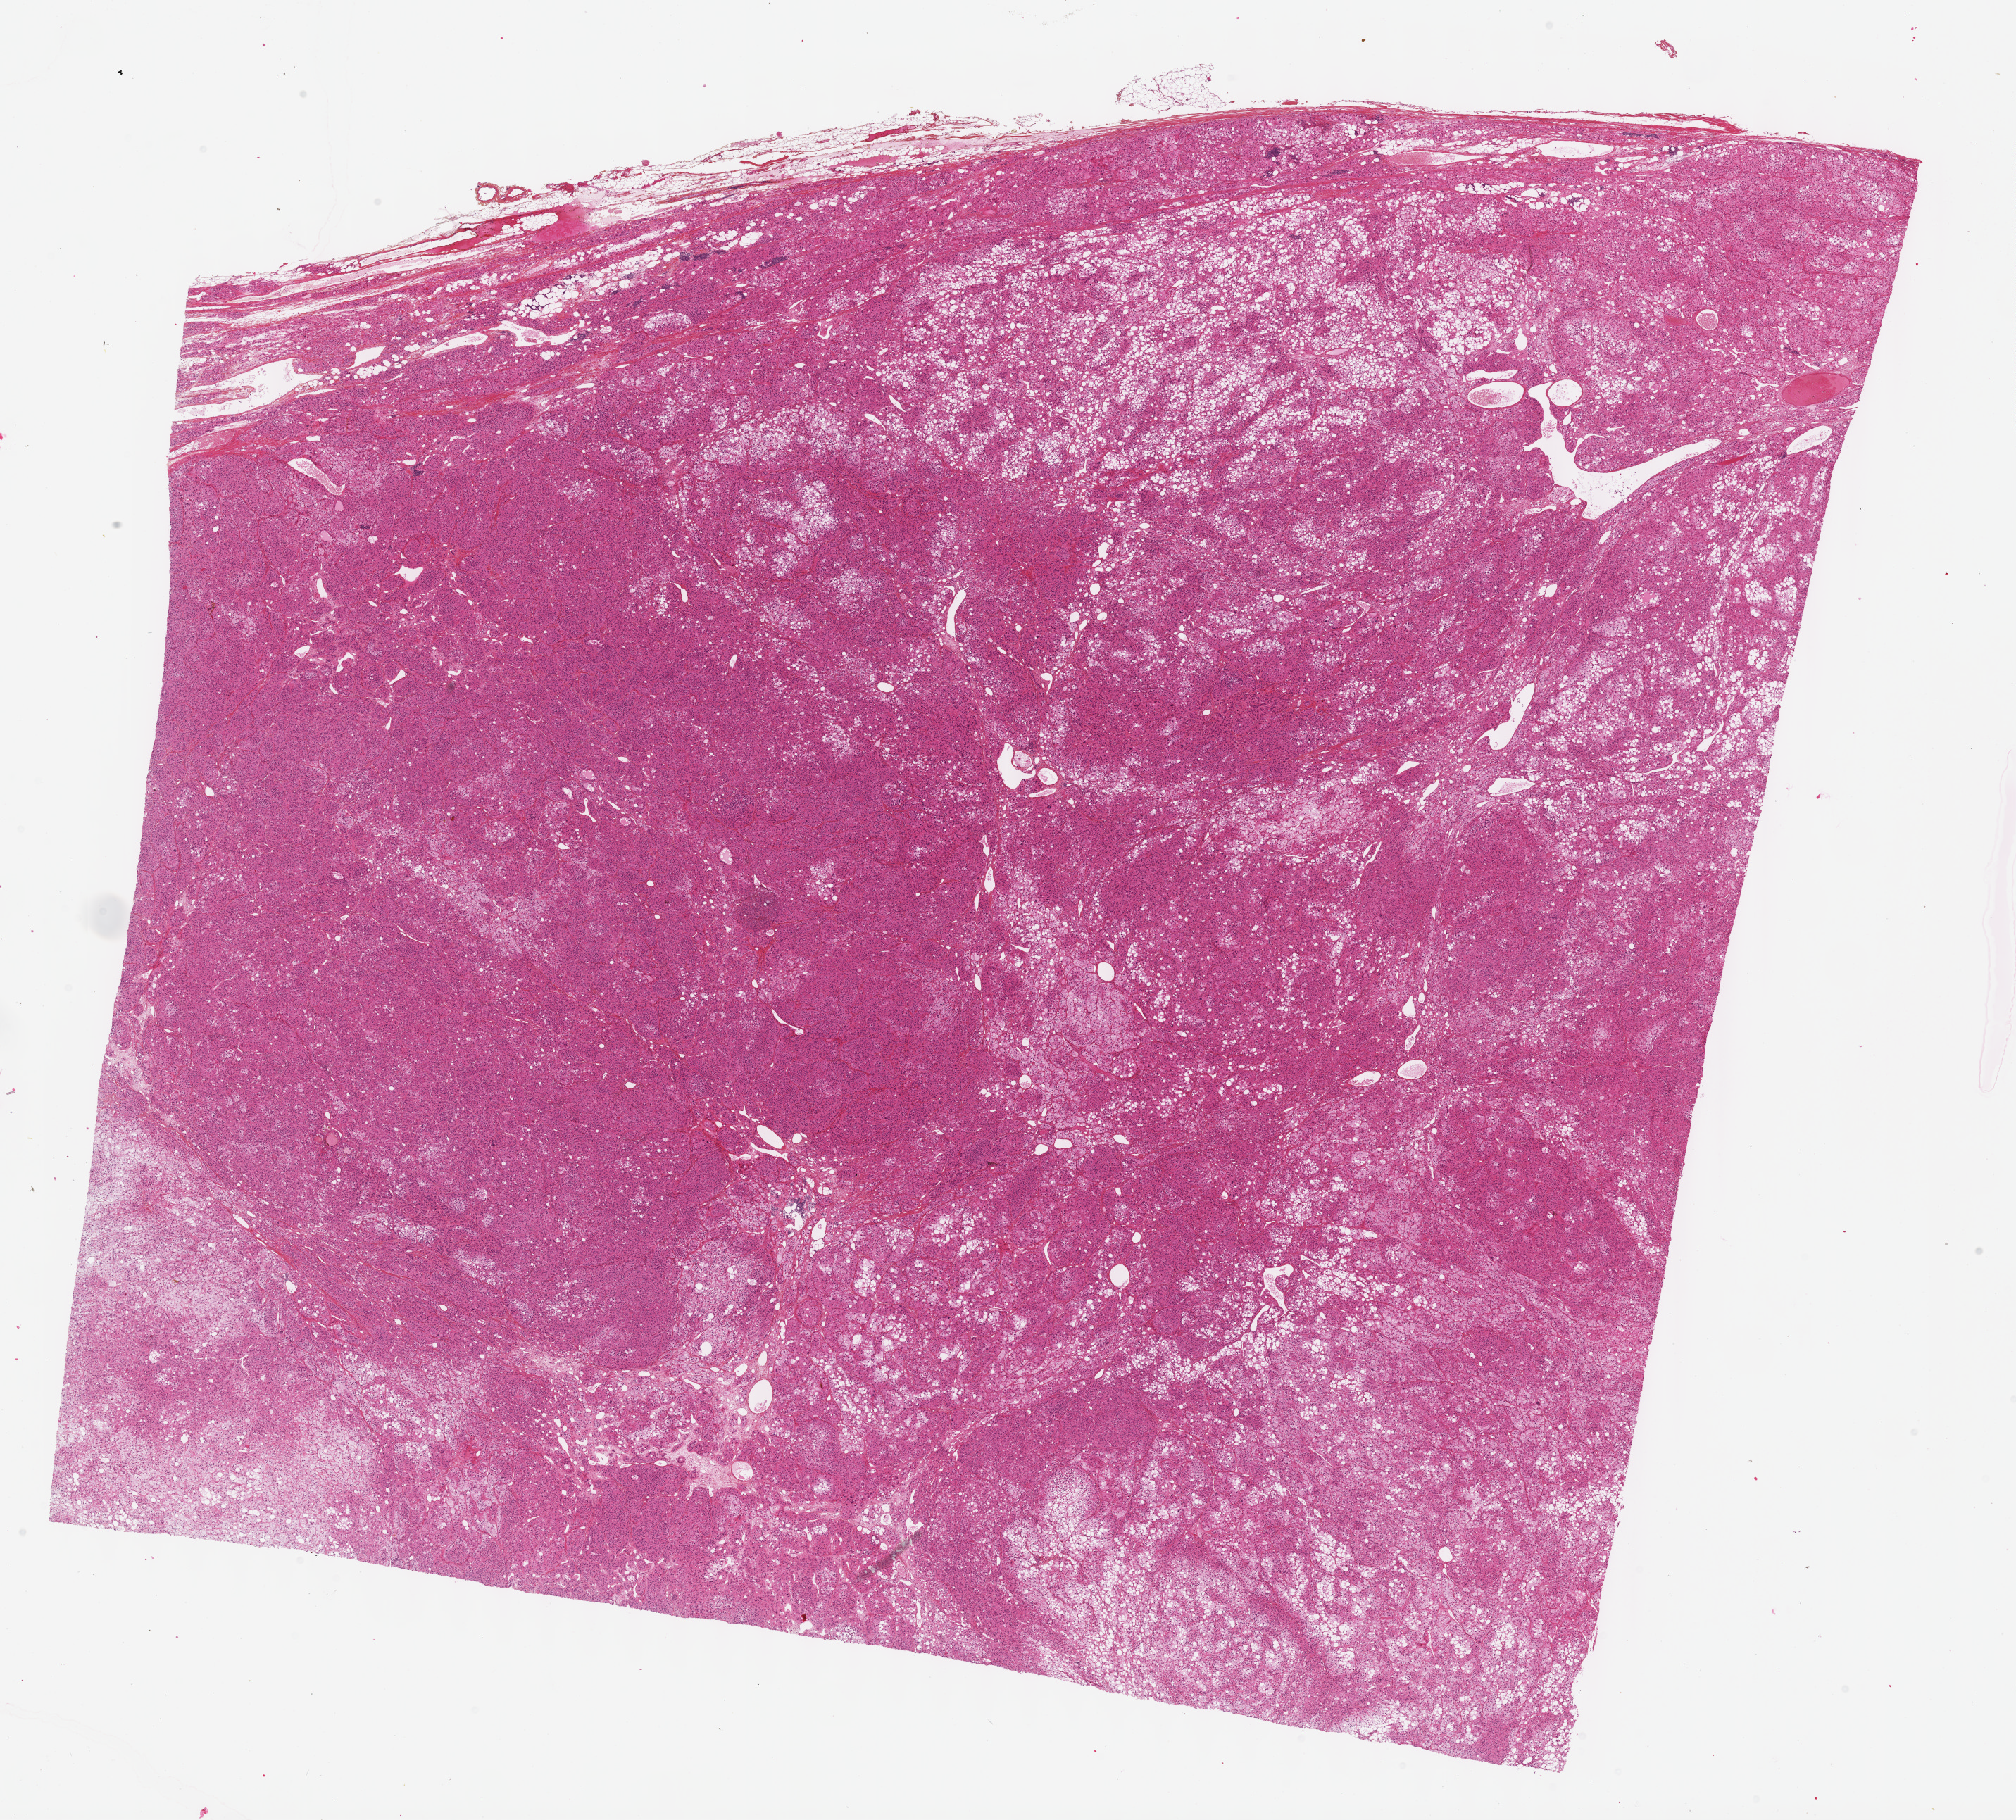
Whole-slide histology image, Hematoxylin and eosin (H&E) stained, a low-resolution overview of the entire scanned area, about 23.1 x 20.9 mm; formalin-fixed paraffin-embedded (FFPE) diagnostic section; primary tumour sample from the adrenal cortex. Female, age 75 years at initial diagnosis.
Histologic diagnosis: Adrenal cortical carcinoma (cortex of adrenal gland).